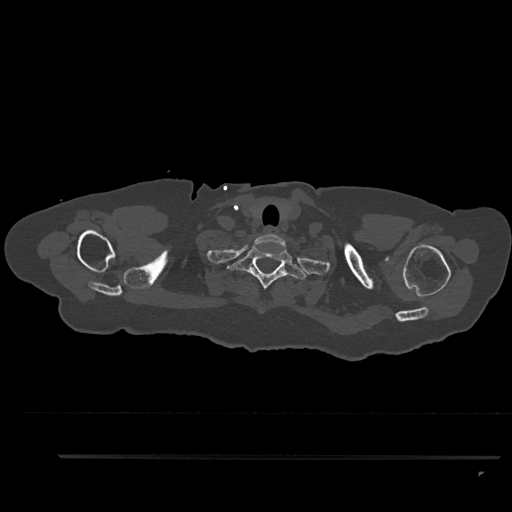
CT including the spine, one axial slice. Position 767 of 797 along the scan axis. Reconstruction kernel Br40s/3. 120 kVp. Bone window (W 1800 / L 400 HU). 512 × 512 image matrix, field of view 408 × 408 mm. Female patient, age 44 years. Case-level facts recorded for this patient, not image findings: primary cancer: renal; vertebrae with lytic lesions (as recorded): L1.
Structures marked on this image (semi-automatic segmentation, software-assisted and operator-edited):
- T1 vertebra: box from (x=226, y=246) to (x=309, y=289) px